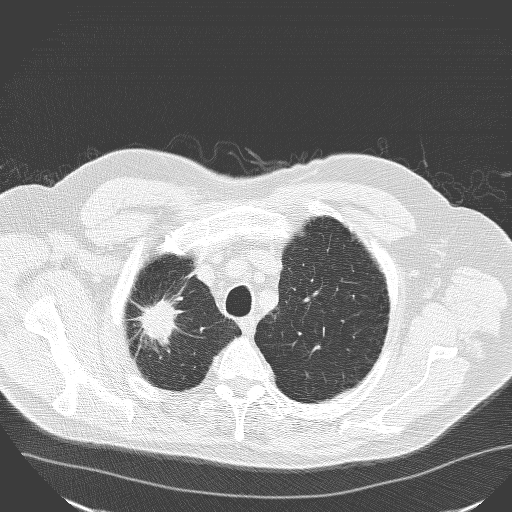
Axial slice from a low-dose chest CT screening exam. First (baseline) screen. Lung window (W 1500 / L -600 HU). Lung (sharp) reconstruction kernel (D). 120 kVp. Slice 138 of 160 in the series. Male, age 71 years at enrolment.
- Expert-annotated lung lesion, box from (x=117, y=284) to (x=189, y=358) px.
- Reader record for this screening exam (exam-level; its link to the box is not recorded): non-calcified nodule or mass ≥4 mm, right upper lobe, 30 × 25 mm, spiculated (stellate) margins, soft tissue attenuation.
- Official screen result: positive, change unspecified: nodule(s) >= 4 mm or enlarging nodule(s), mass(es), or other non-specific abnormalities suspicious for lung cancer.
- Later outcome: lung cancer diagnosed 182 days after this screen — squamous cell carcinoma, NOS, right upper lobe, poorly differentiated (G3), stage IA (AJCC 6th edition), 30 mm at pathology.